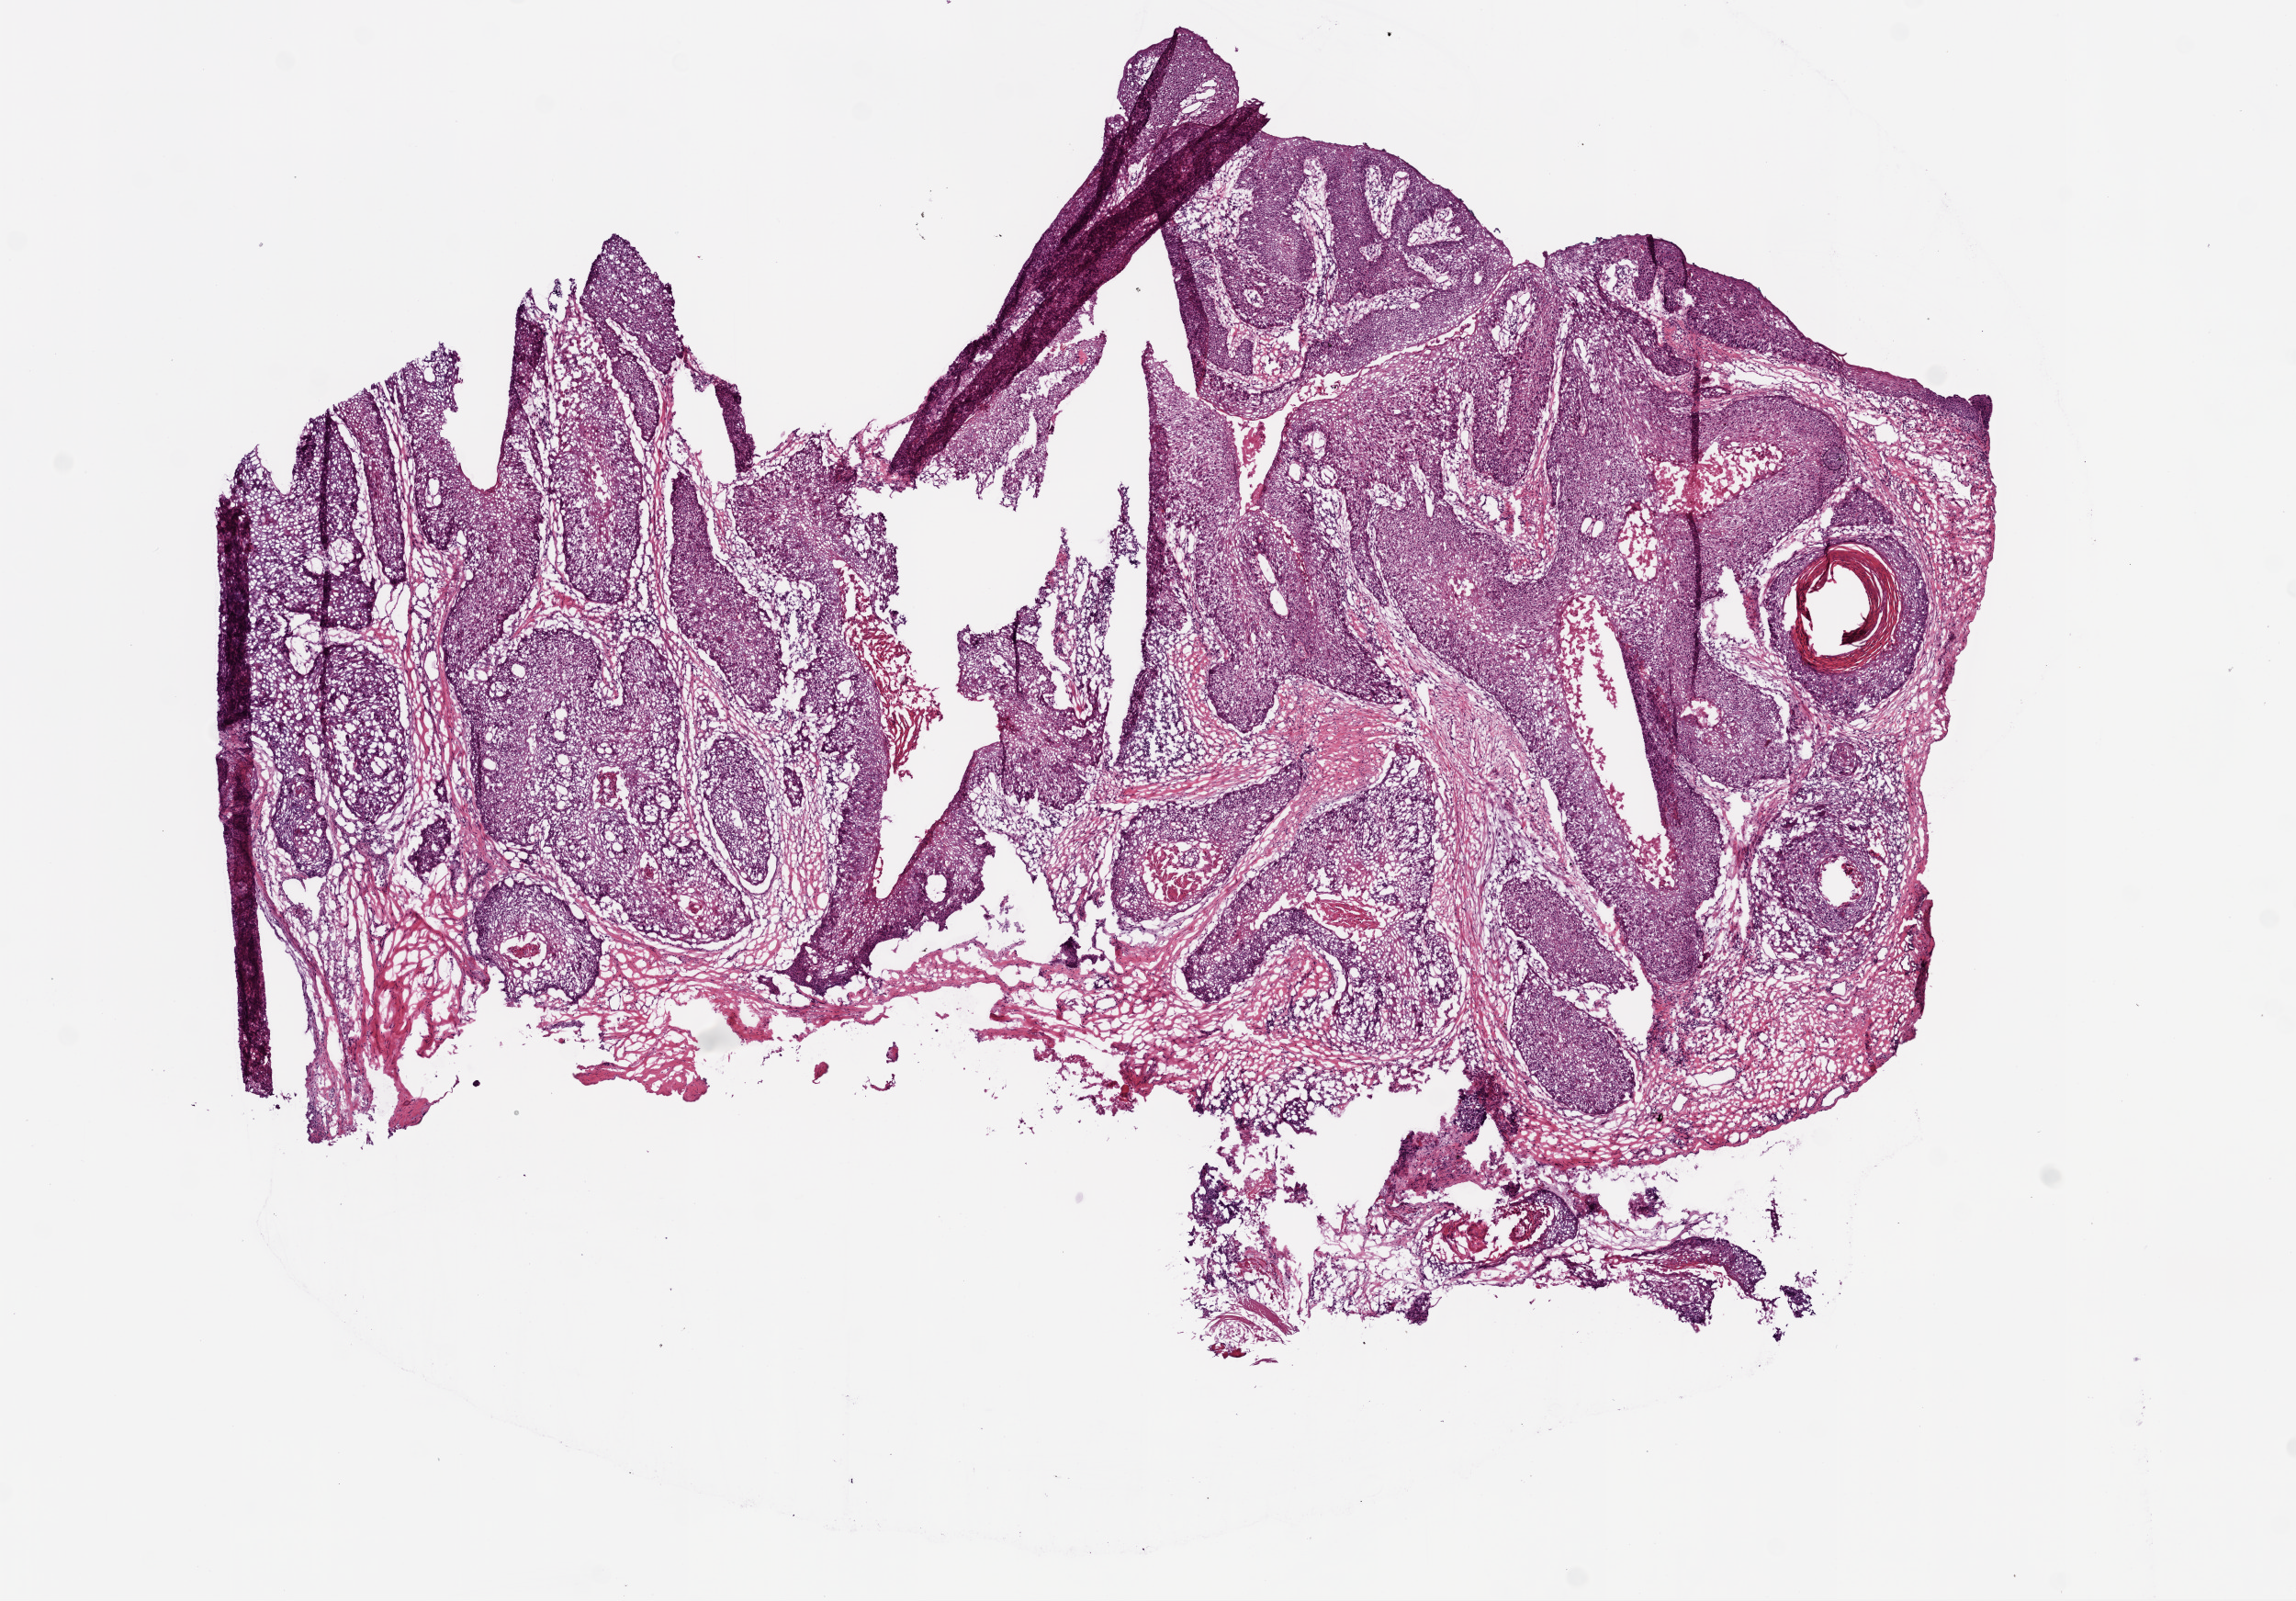
Whole-slide histology image, Hematoxylin and eosin (H&E) stained, whole scanned area (about 10.0 x 7.0 mm) shown as a low-resolution overview. Frozen section. Sample: primary tumour, head and neck. Male, age 75 years at initial diagnosis.
Diagnosis: Squamous cell carcinoma, NOS (gum, NOS).